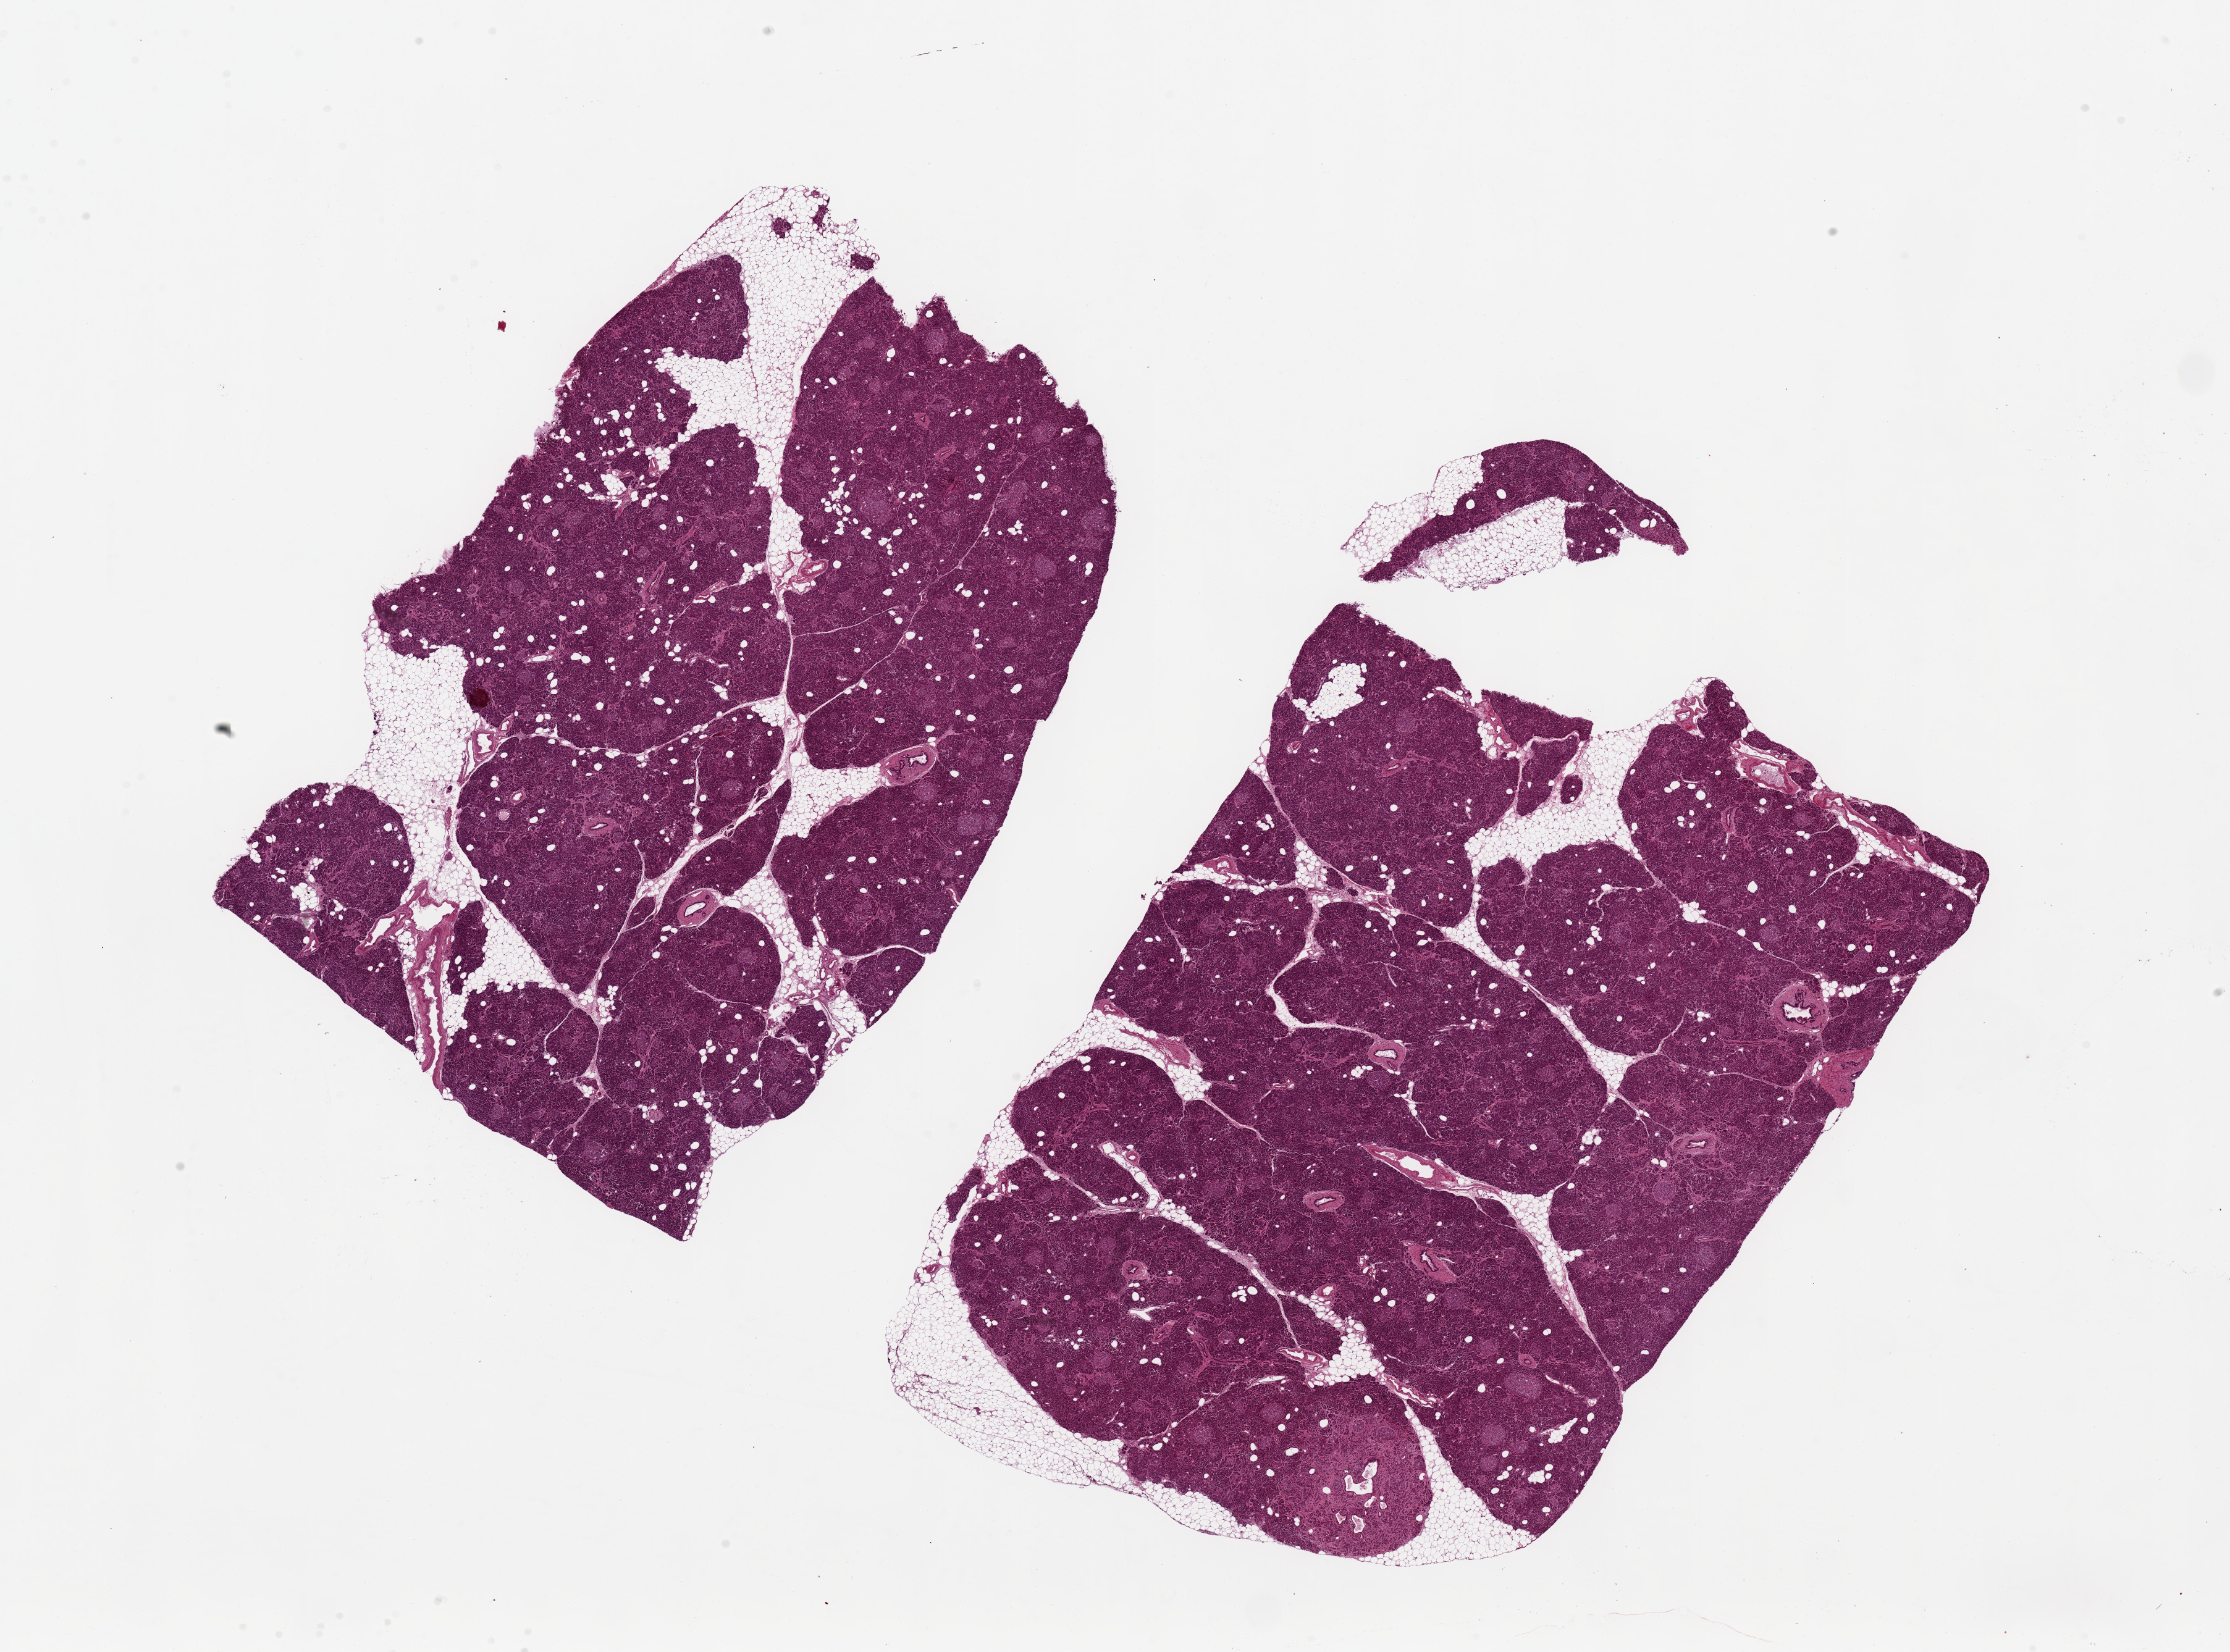
Whole-slide image, haematoxylin and eosin stain — a low-resolution overview of the entire scanned area, about 28.5 x 21.2 mm, PAXgene-fixed, paraffin-embedded tissue, target tissue: pancreas, donor tissue sample. Donor sex: female.
Review note (as recorded): 2 pieces, 12x8.5 & 15x9mm; numerous well-defined Islets.